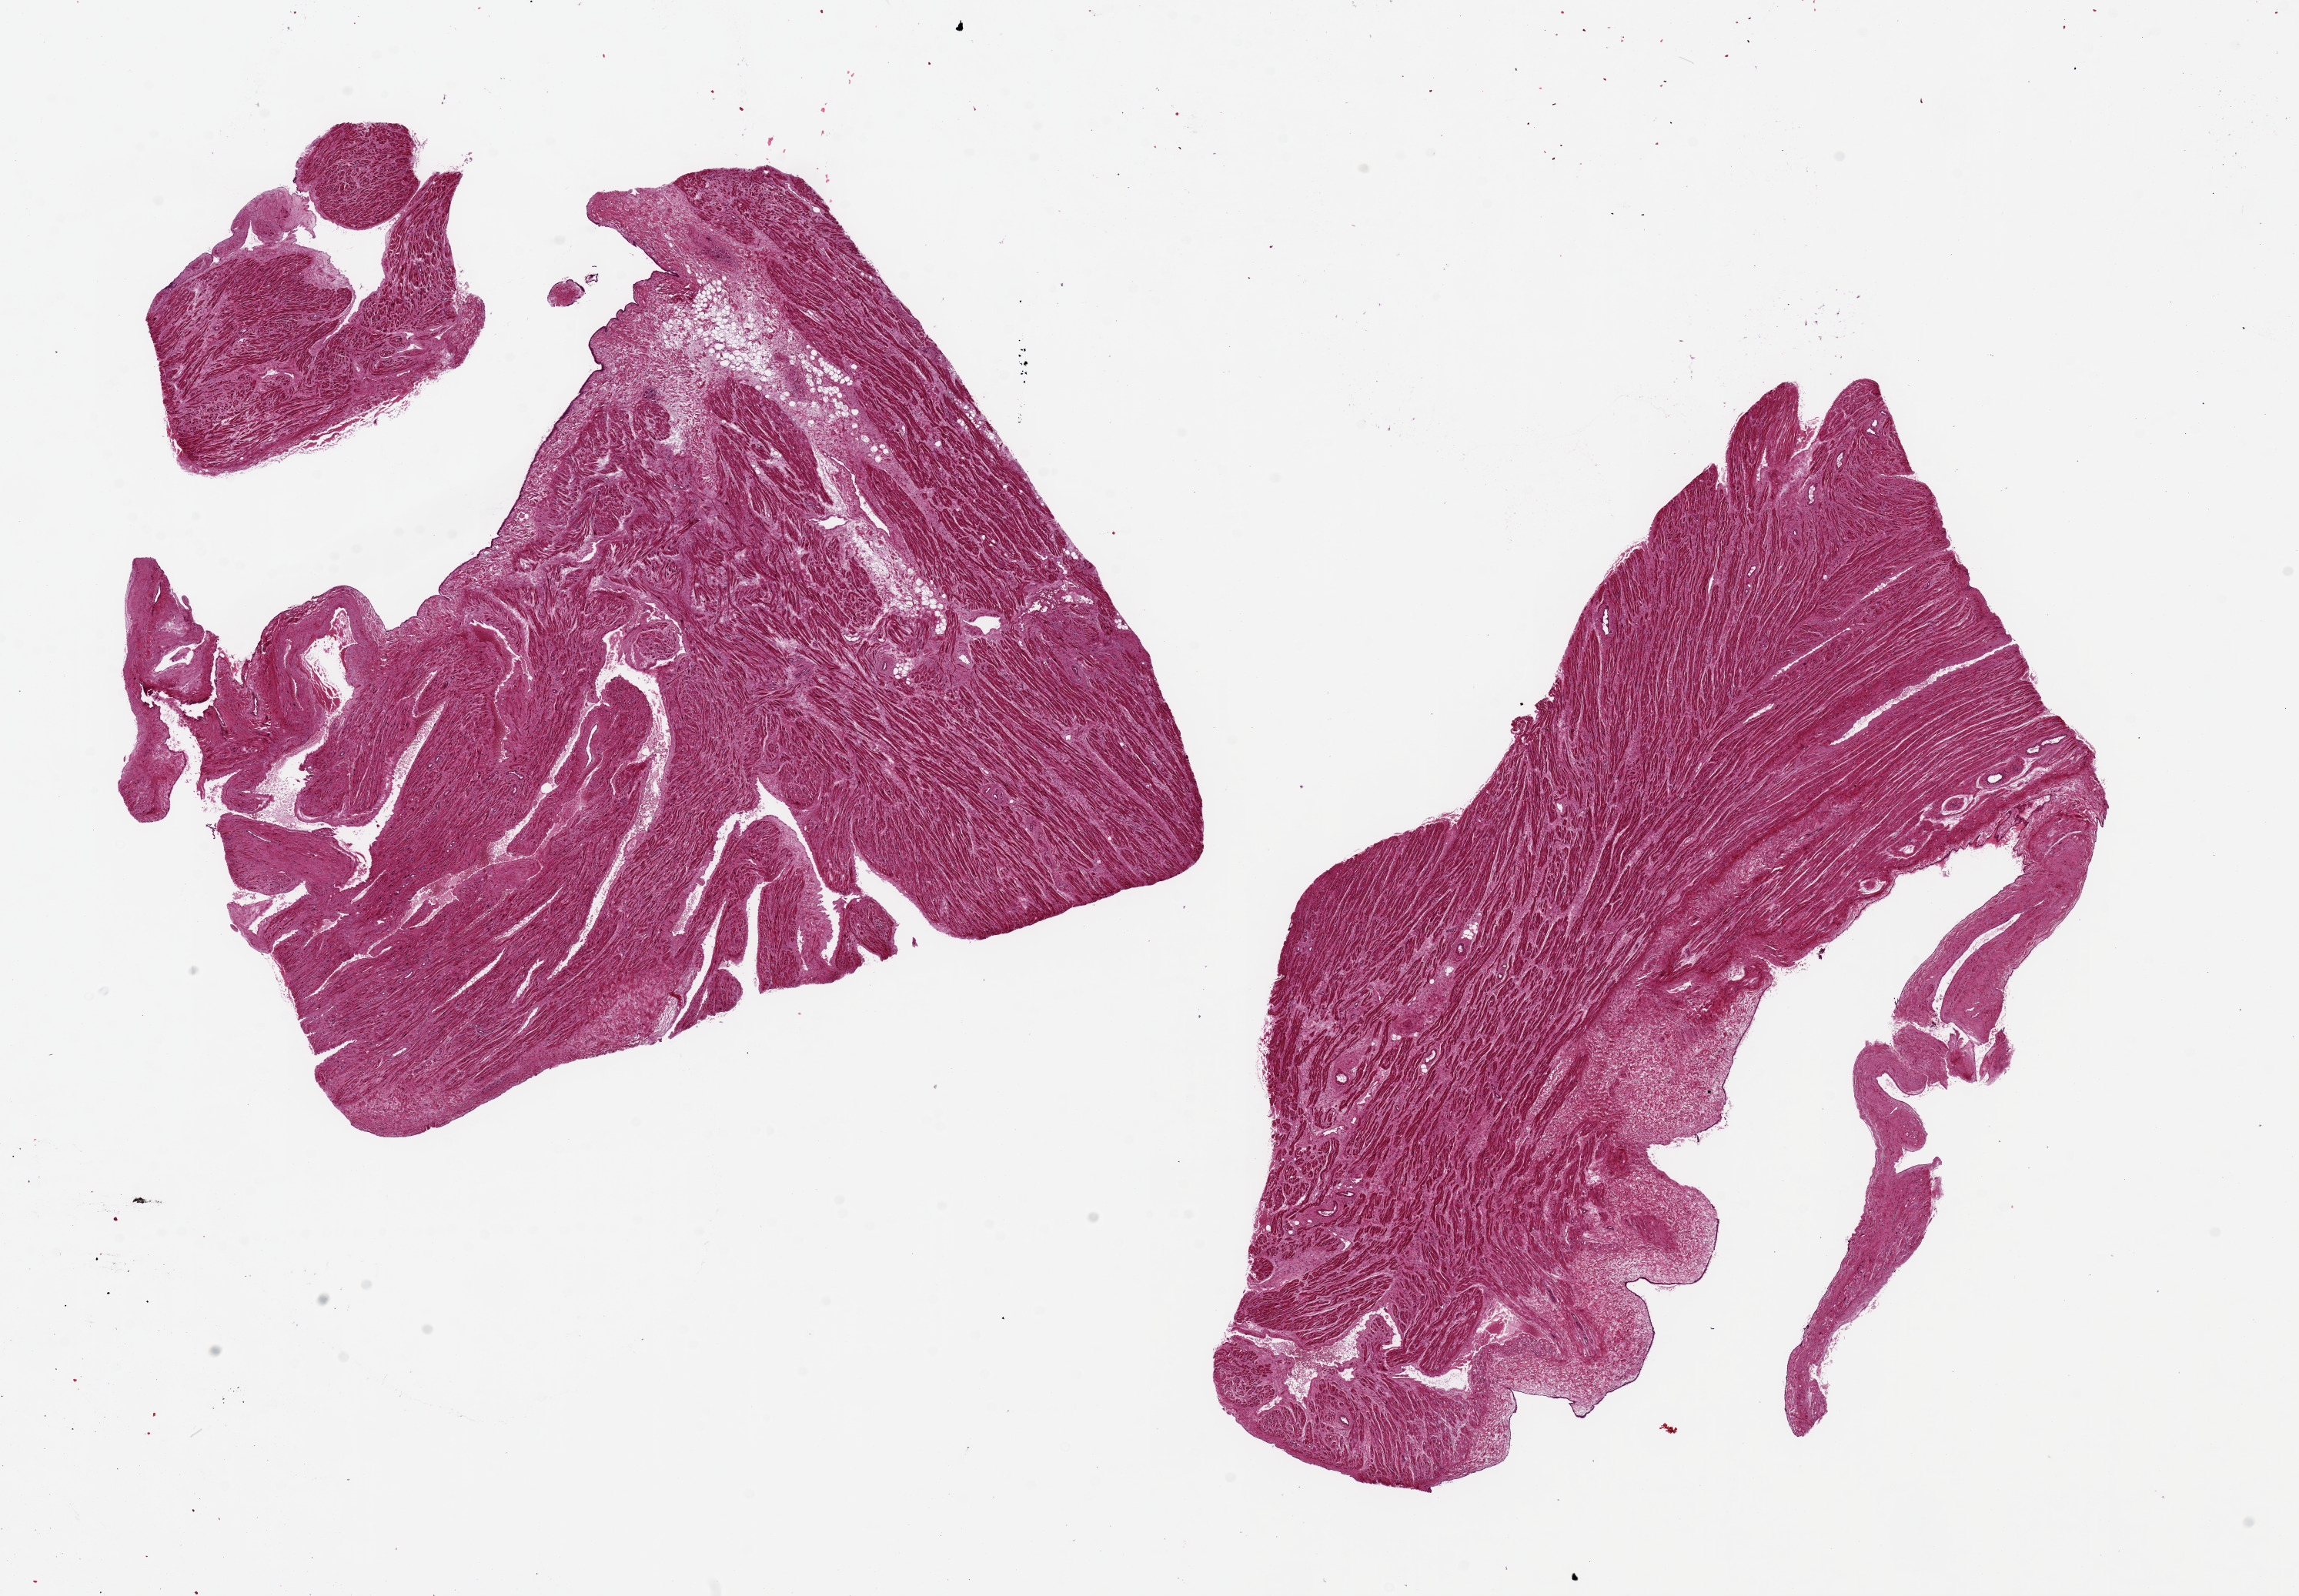
Whole-slide image, haematoxylin and eosin stain, brightfield, low-resolution overview of the scanned area, about 23.6 x 16.4 mm; PAXgene-fixed, paraffin-embedded tissue; target tissue: auricular appendage; tissue donor sample. Male donor.
* pathologist's review note for this sample: 2 pieces ~ !0x6mm